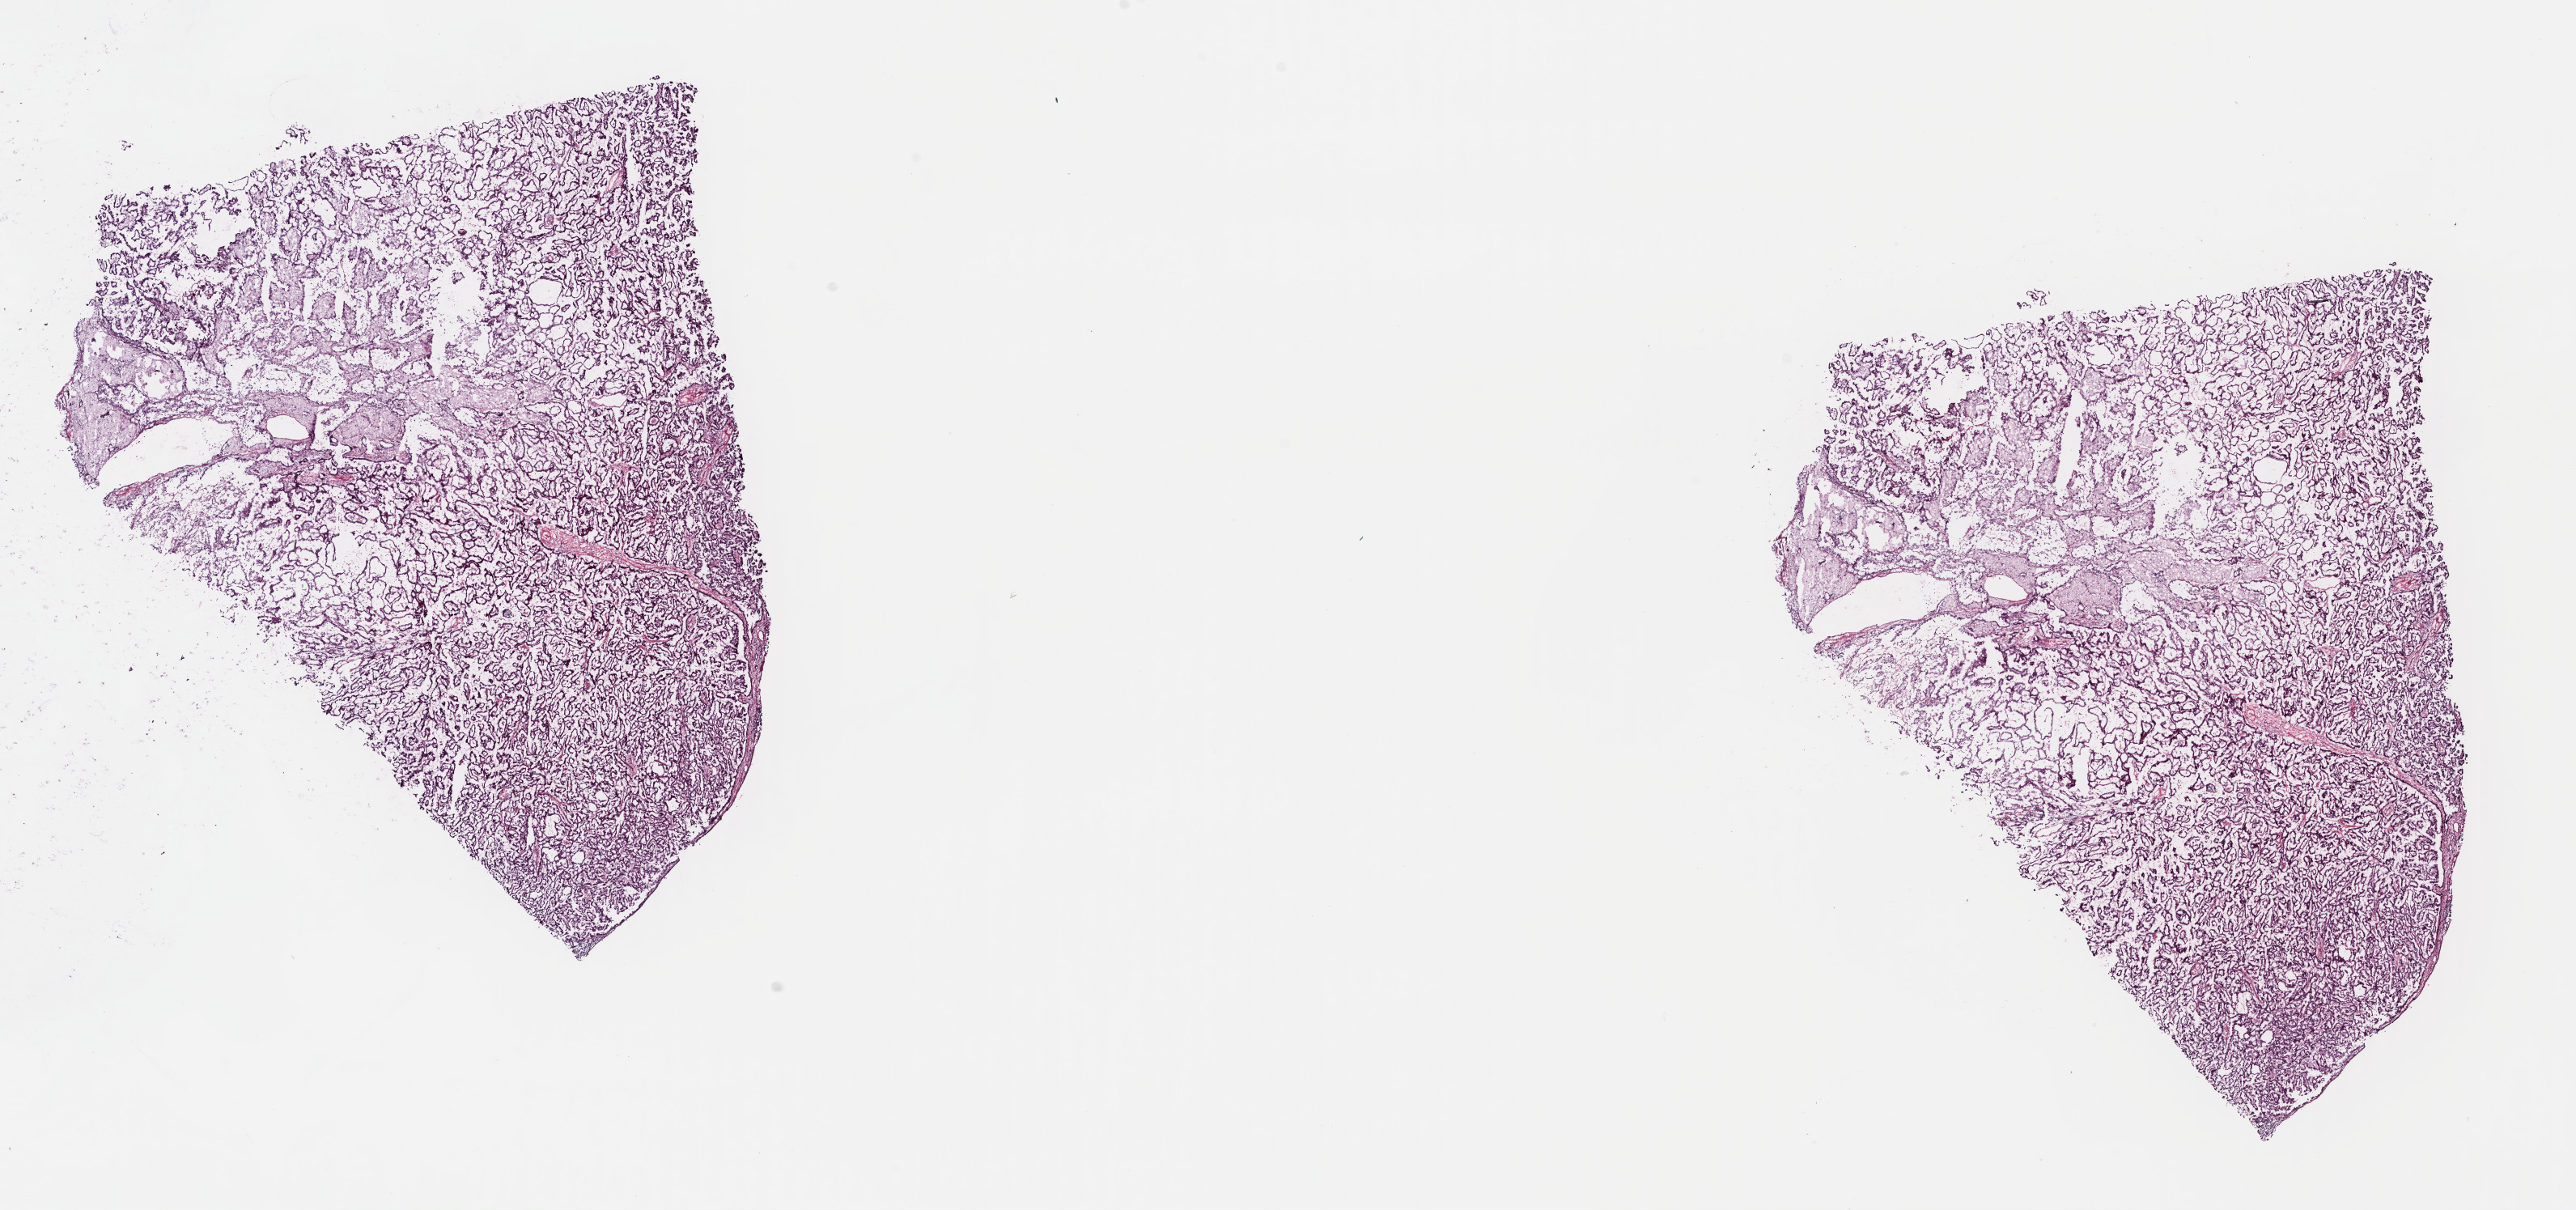
H&E-stained whole-slide image, shown as a low-resolution overview of the whole scanned area (about 25.0 x 11.8 mm). Frozen section. Primary tumour sample from the kidney. Male patient; age at initial diagnosis 40 years. Slide review estimates, as recorded: tumour cells 75%, tumour nuclei 75%, normal cells 0%, stromal cells 25%, necrosis 0%. Infiltration values recorded for this section: lymphocyte infiltration 2%, monocyte infiltration 5%, neutrophil infiltration 2%.
- AJCC pathologic stage: I (7th edition)
- pathologic diagnosis: Papillary adenocarcinoma, NOS